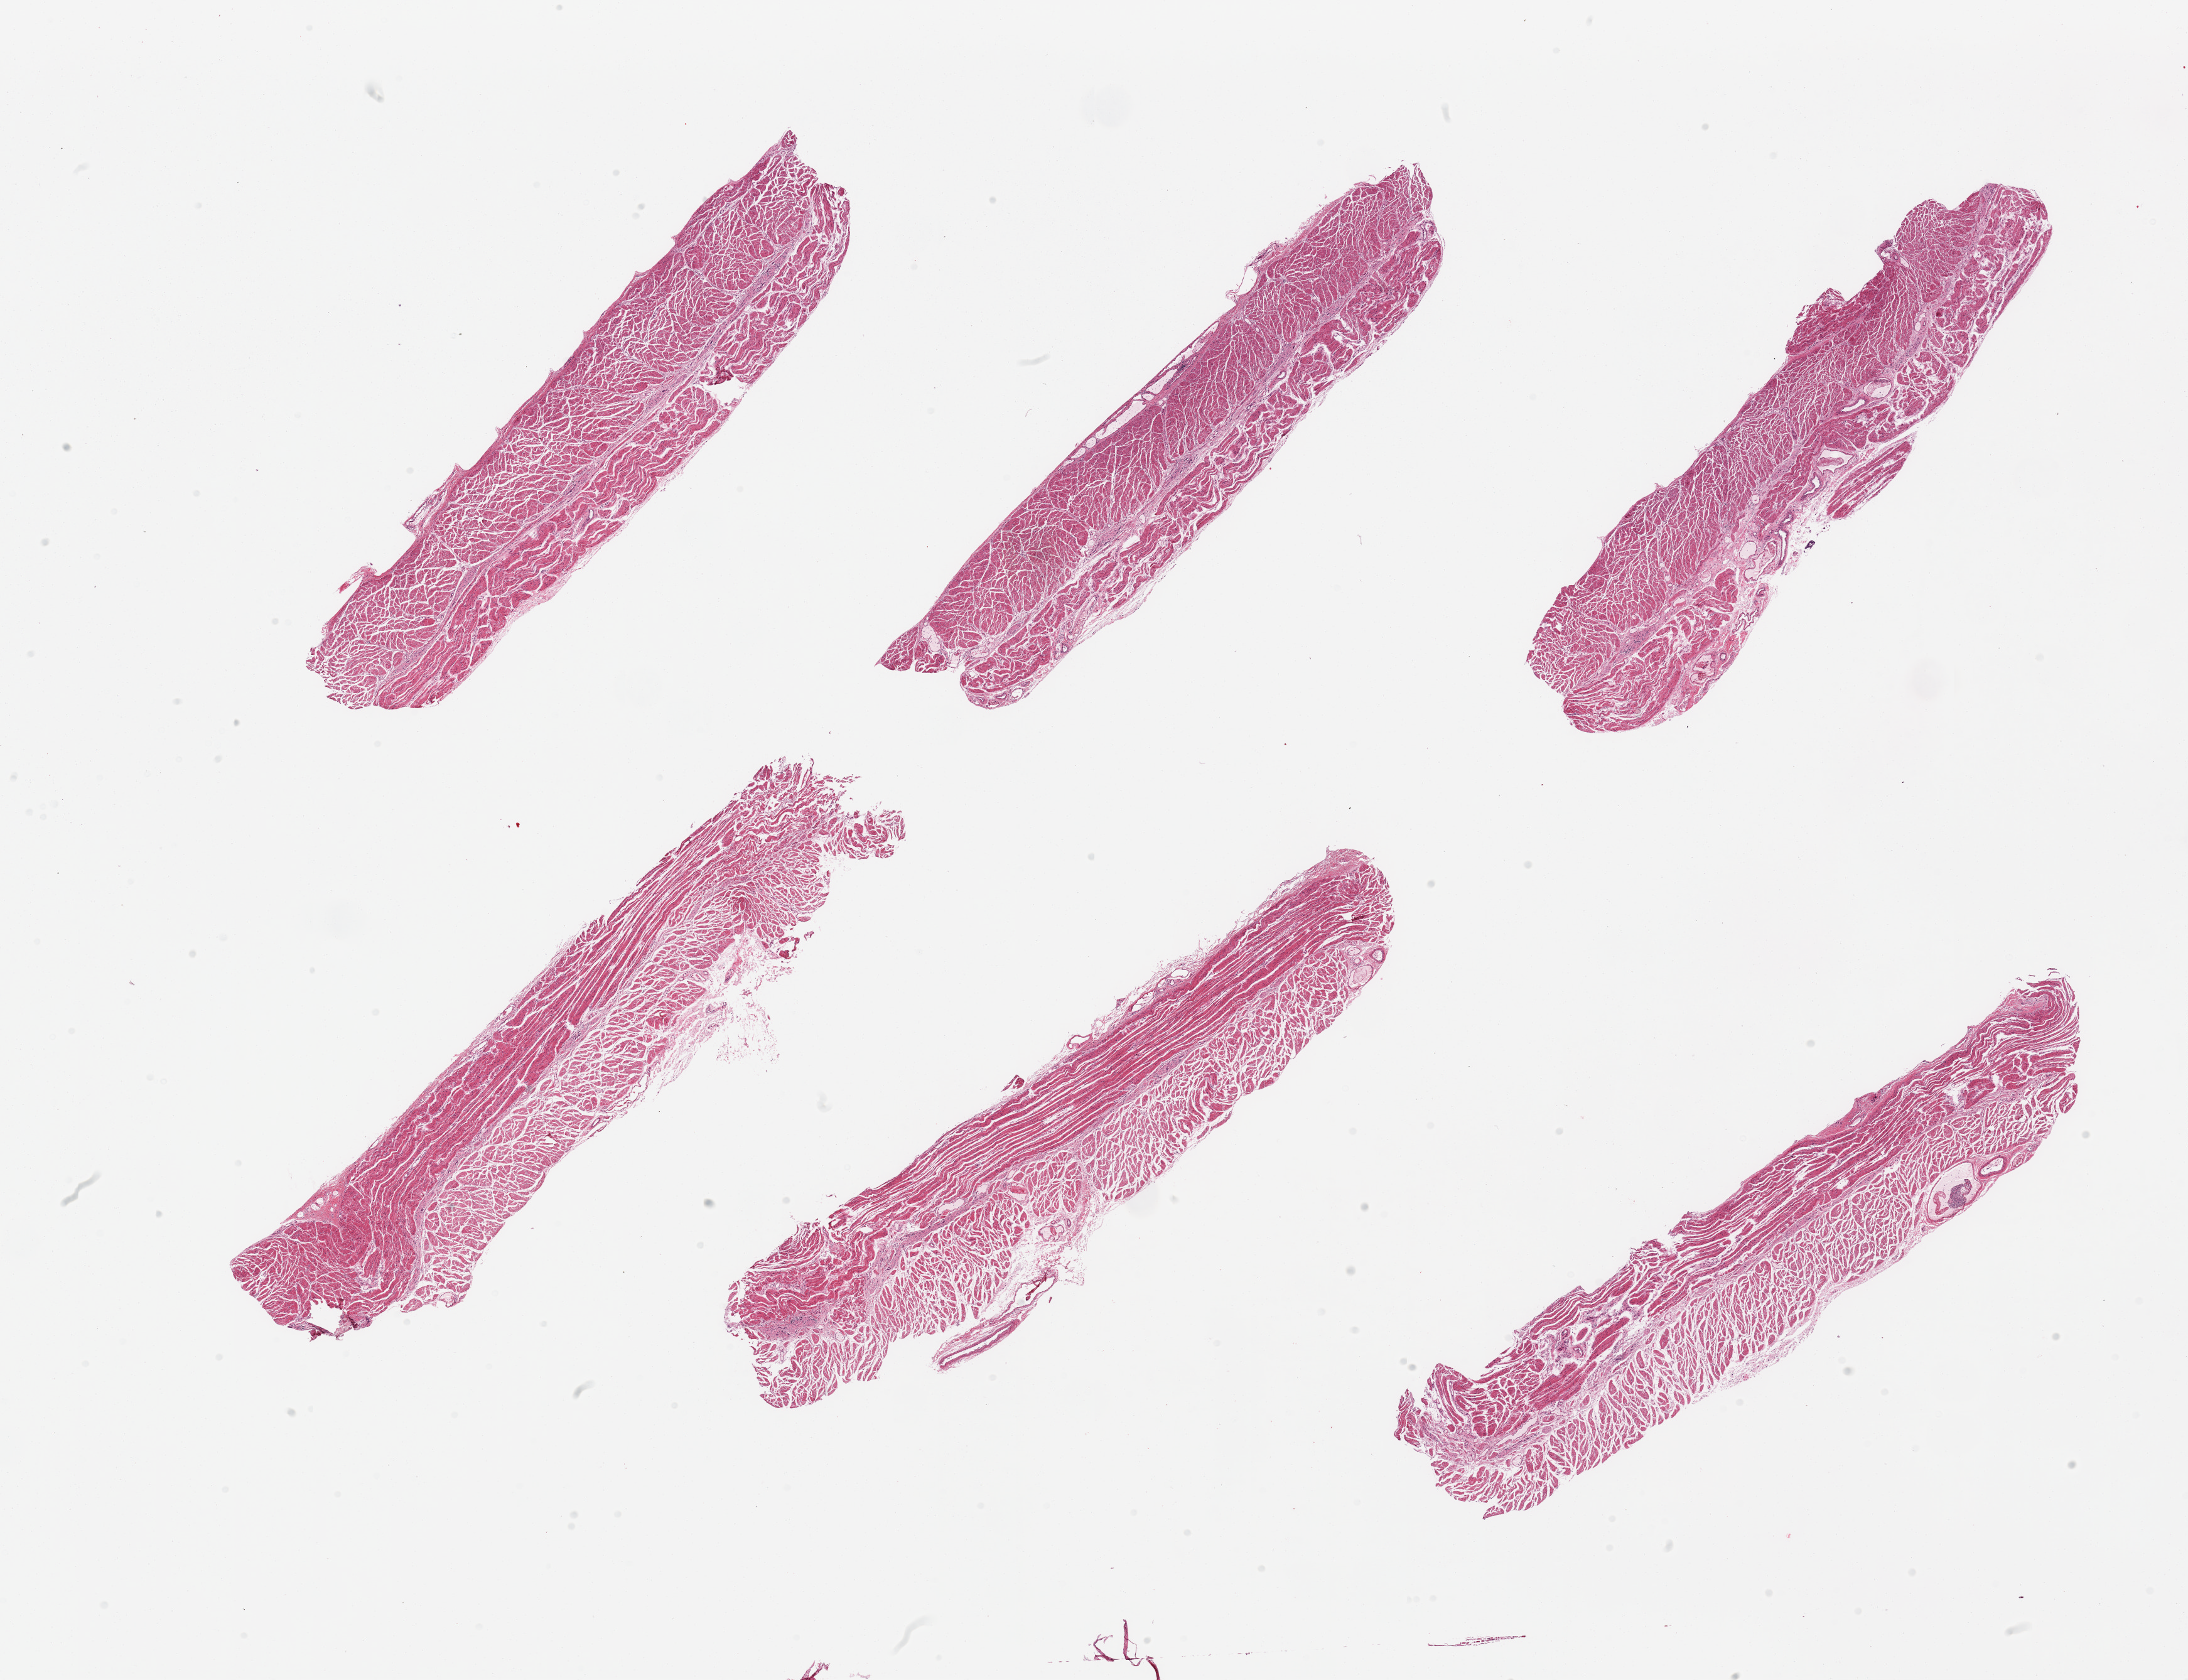
Whole-slide image, haematoxylin and eosin stain, brightfield — low-resolution overview of the scanned area, about 27.6 x 21.2 mm (from a 20x scan). PAXgene-fixed paraffin-embedded (PFPE) section. Sampled site (target tissue): gastroesophageal junction. Donor tissue sample.
Reviewer comment on this tissue sample: 6 pieces, target muscularis, good specimen.